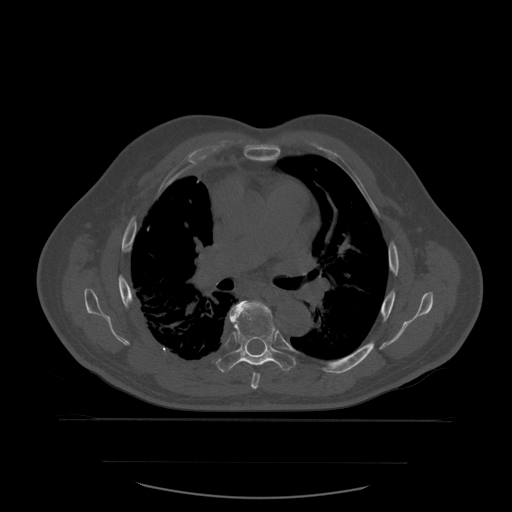
CT including the spine, one axial slice; position 389 of 590 along the scan axis; bone window (W 1800 / L 400 HU); 512 × 512 image matrix, field of view 479 × 479 mm. Patient age 71 years. Case-level facts recorded for this patient, not image findings: primary cancer: lung.
Outlined on this slice (semi-automatically segmented with operator editing):
- T6 vertebra: bounding box <246,301,261,389> (left, top, right, bottom; pixels)
- T7 vertebra: <216,301,297,373>